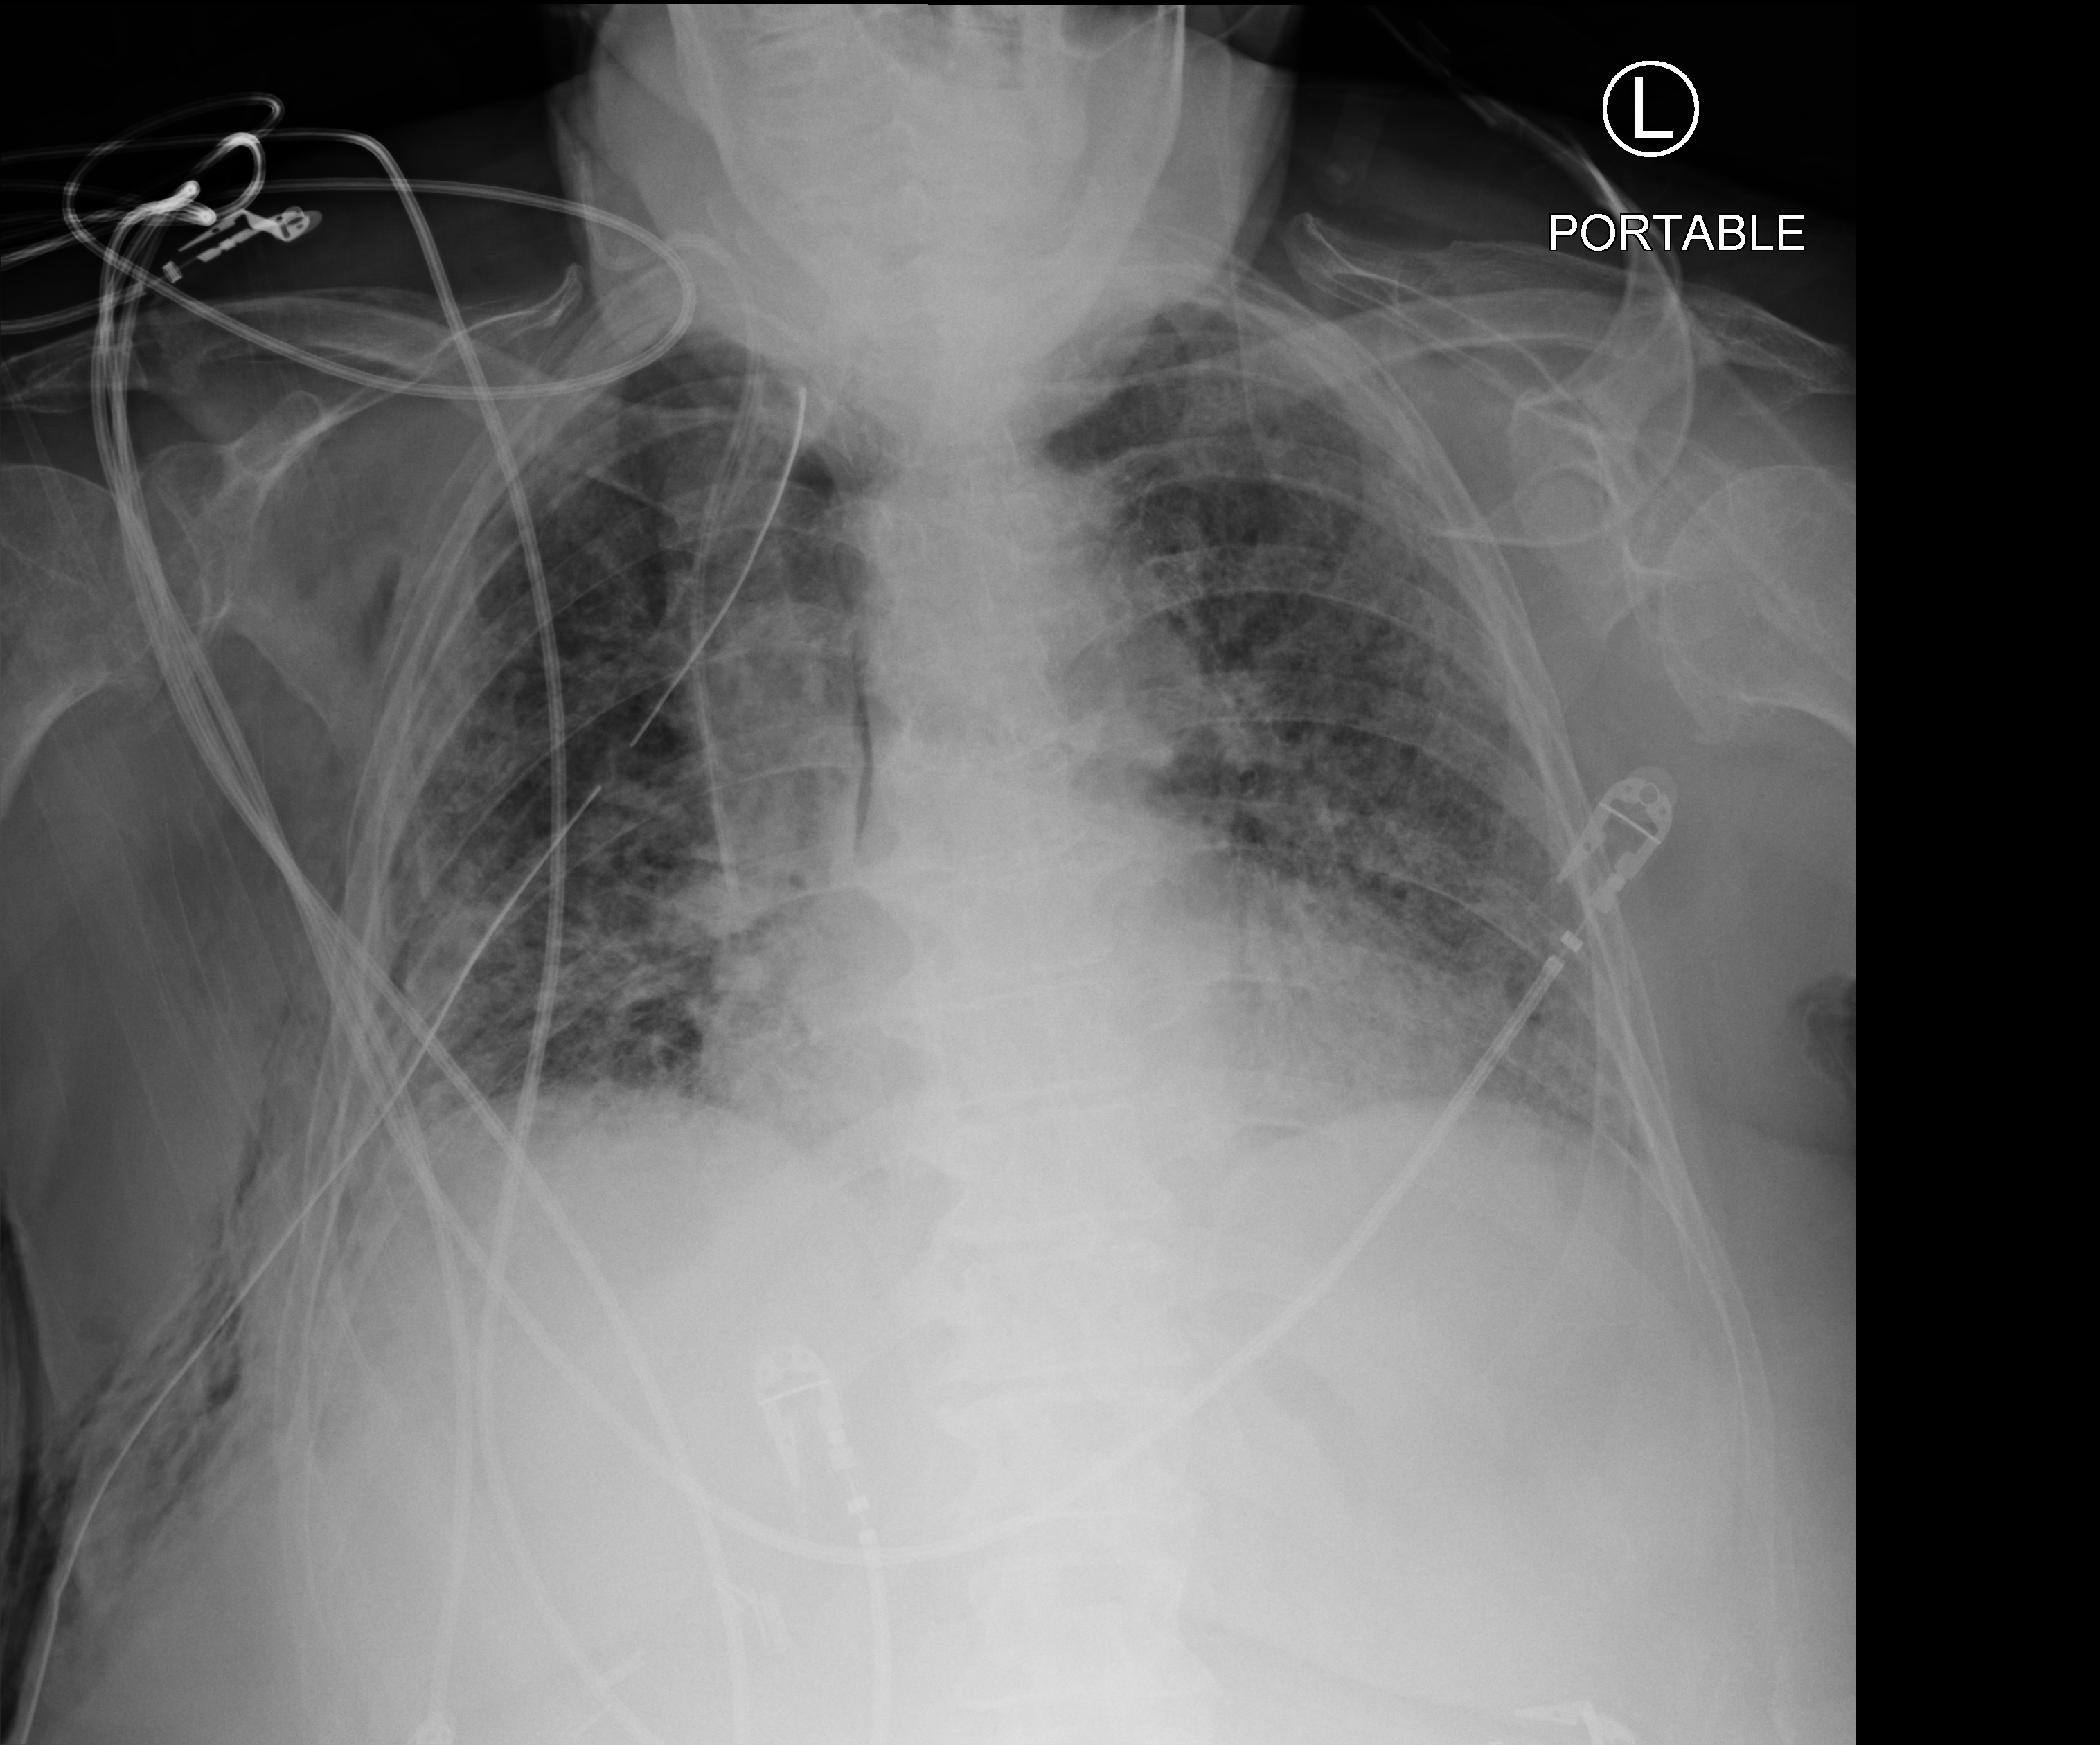
Chest X-ray (portable). Female patient hospitalised with COVID-19, age 75–90 years.
Admission-level facts for this patient (not findings on this image; timing relative to this image not recorded): mechanically ventilated during this hospital stay: yes; length of hospital stay: 56 days.